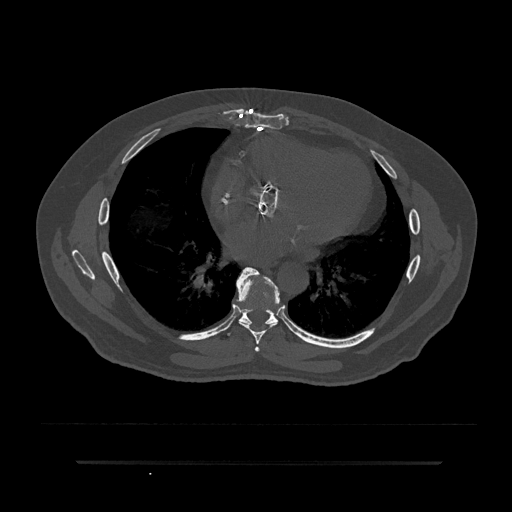
CT including the spine, one axial slice; position 457 of 797 along the scan axis; reconstruction kernel Br40s/3; bone window (W 1800 / L 400 HU); 512 × 512 image matrix. Patient: male, 59 years. From the clinical record (not read from this slice): primary cancer: bile ducts; vertebrae with lytic lesions (as recorded): T10.
Outlined on this slice (semi-automatic segmentation, software-assisted and operator-edited):
- T6 vertebra: bounding box <254,347,260,352> (left, top, right, bottom; pixels)
- T7 vertebra: <234,267,280,344>
- T8 vertebra: <221,308,296,335>